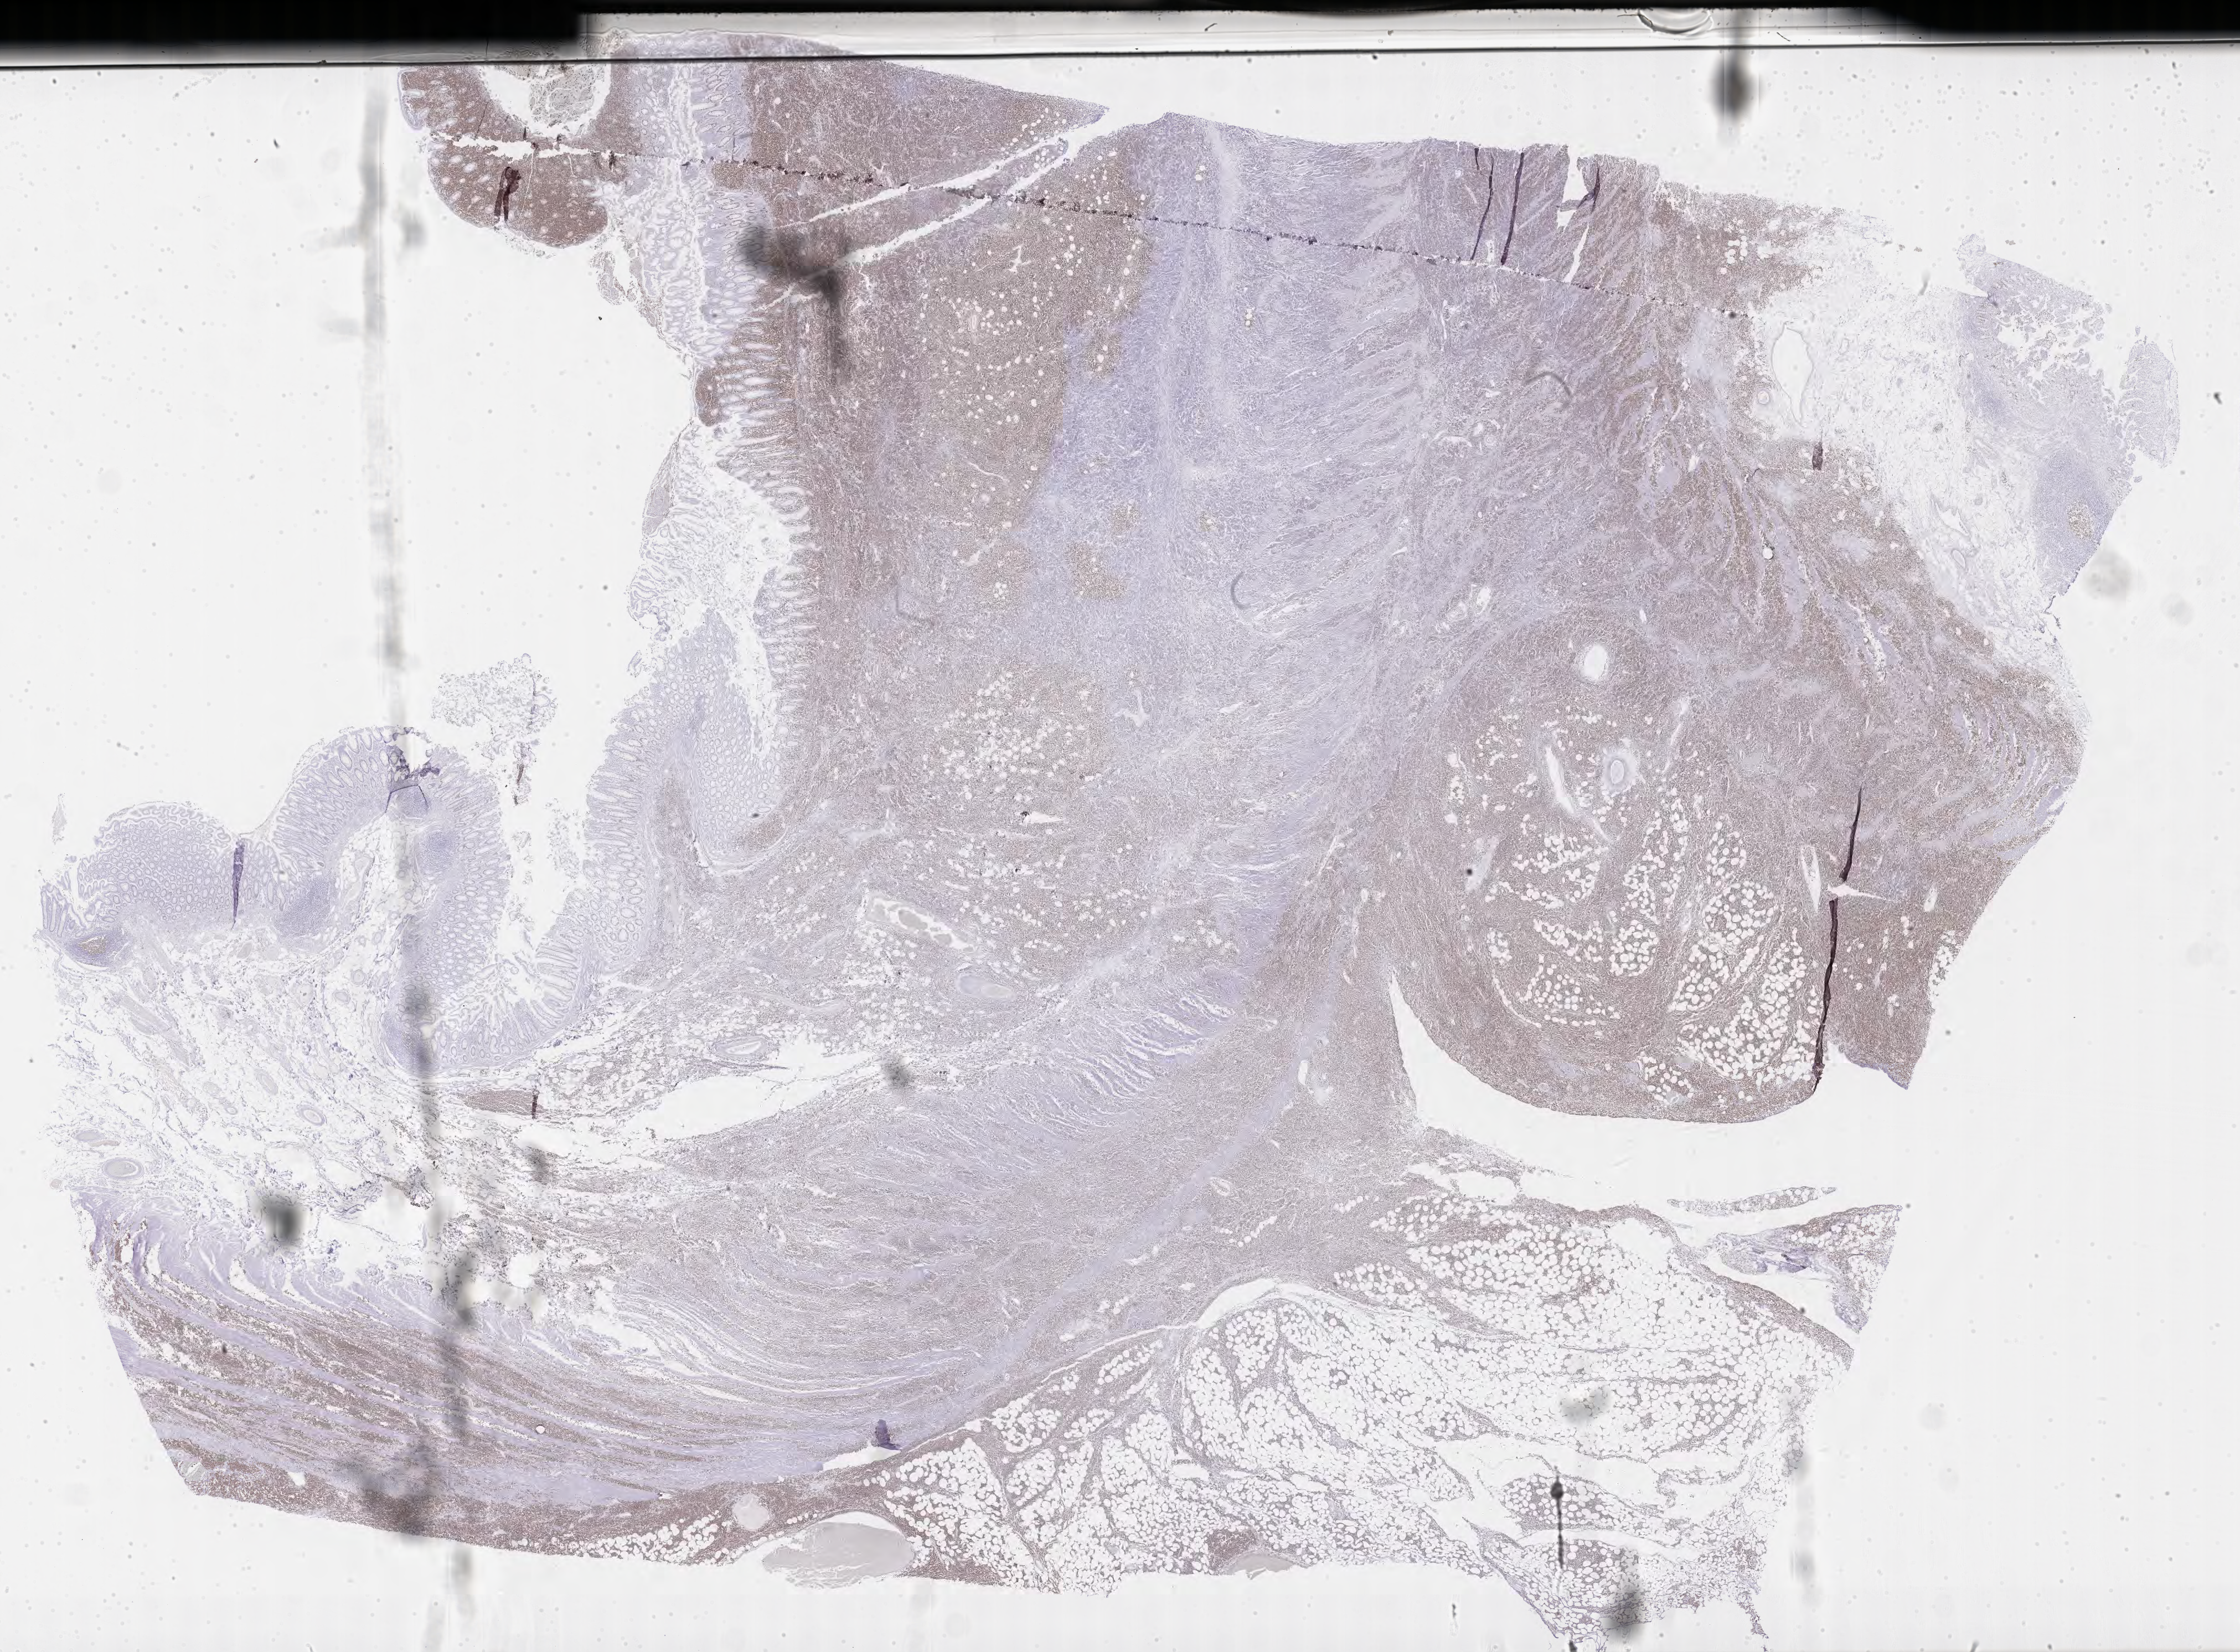
Whole-slide image, immunohistochemical stain for Ki-67 — a low-resolution overview of the entire scanned area, about 32.7 x 24.1 mm. Tumor tissue. Male patient, age 56 years.
Histologic diagnosis: Burkitt lymphoma, NOS.